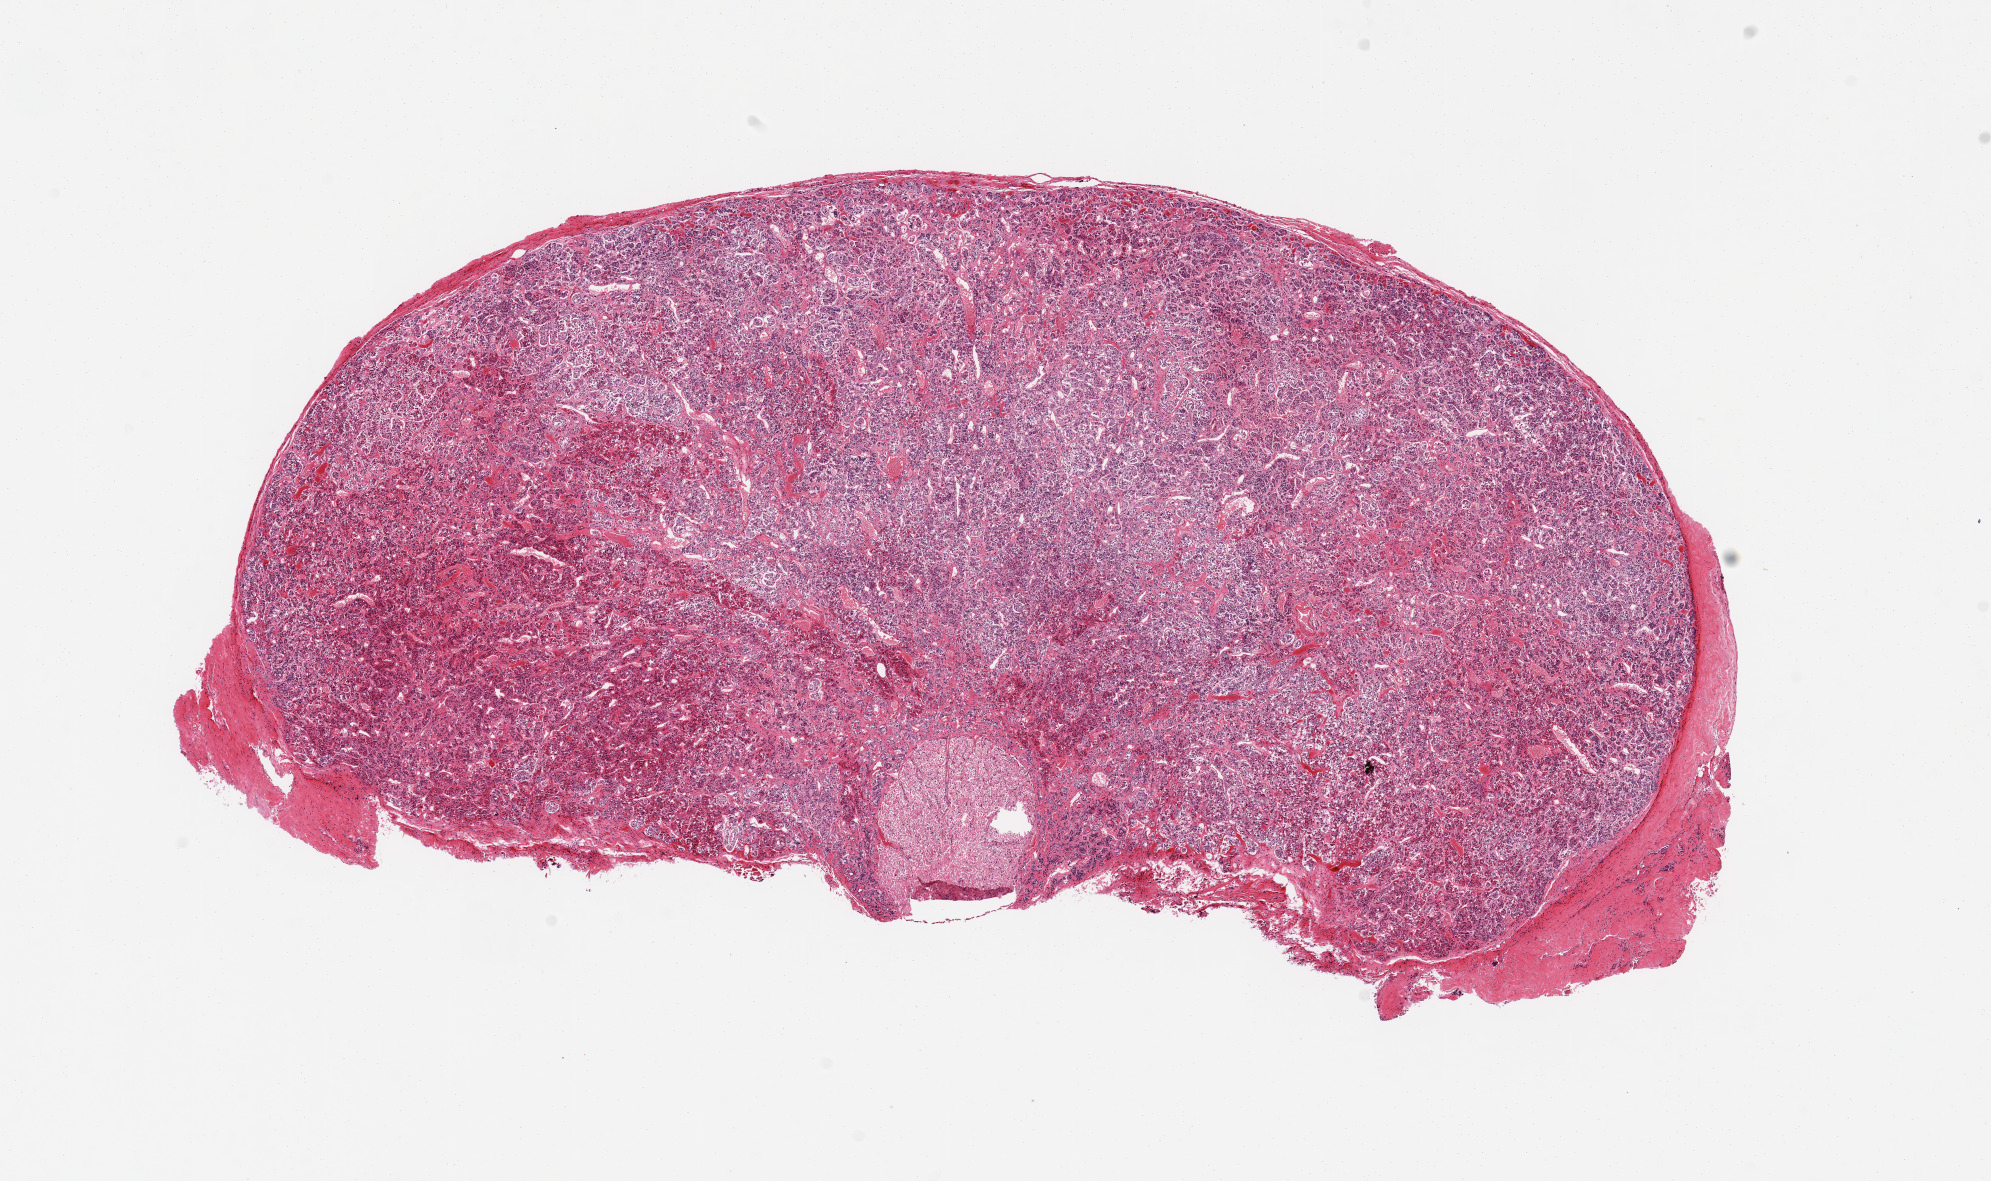
Digitized hematoxylin and eosin (H&E)-stained section, brightfield, whole scanned area (about 15.8 x 9.3 mm) shown as a low-resolution overview; PAXgene-fixed, paraffin-embedded tissue; target tissue: pituitary; tissue donor sample.
Pathologist's review note for this sample: 1 piece; mostly anterior; posterior labeled.